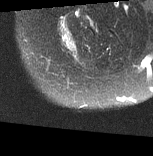
MRI of an extremity soft-tissue mass, one axial slice; T2-weighted fat-saturated; MR volume resampled by the dataset authors to the PET/CT grid (not the native acquisition matrix); 3.27 mm slice thickness; 153 × 156 image matrix, field of view 149 × 152 mm. Female patient. From the clinical record (not read from this slice): histological type: synovial sarcoma; grade: intermediate; site of the primary tumour: right buttock.
Outlined on this slice (expert contour drawn on MRI and transferred to this co-registered scan by the dataset authors):
- gross tumour volume including surrounding oedema: bounding box <58,18,77,57> (left, top, right, bottom; pixels)